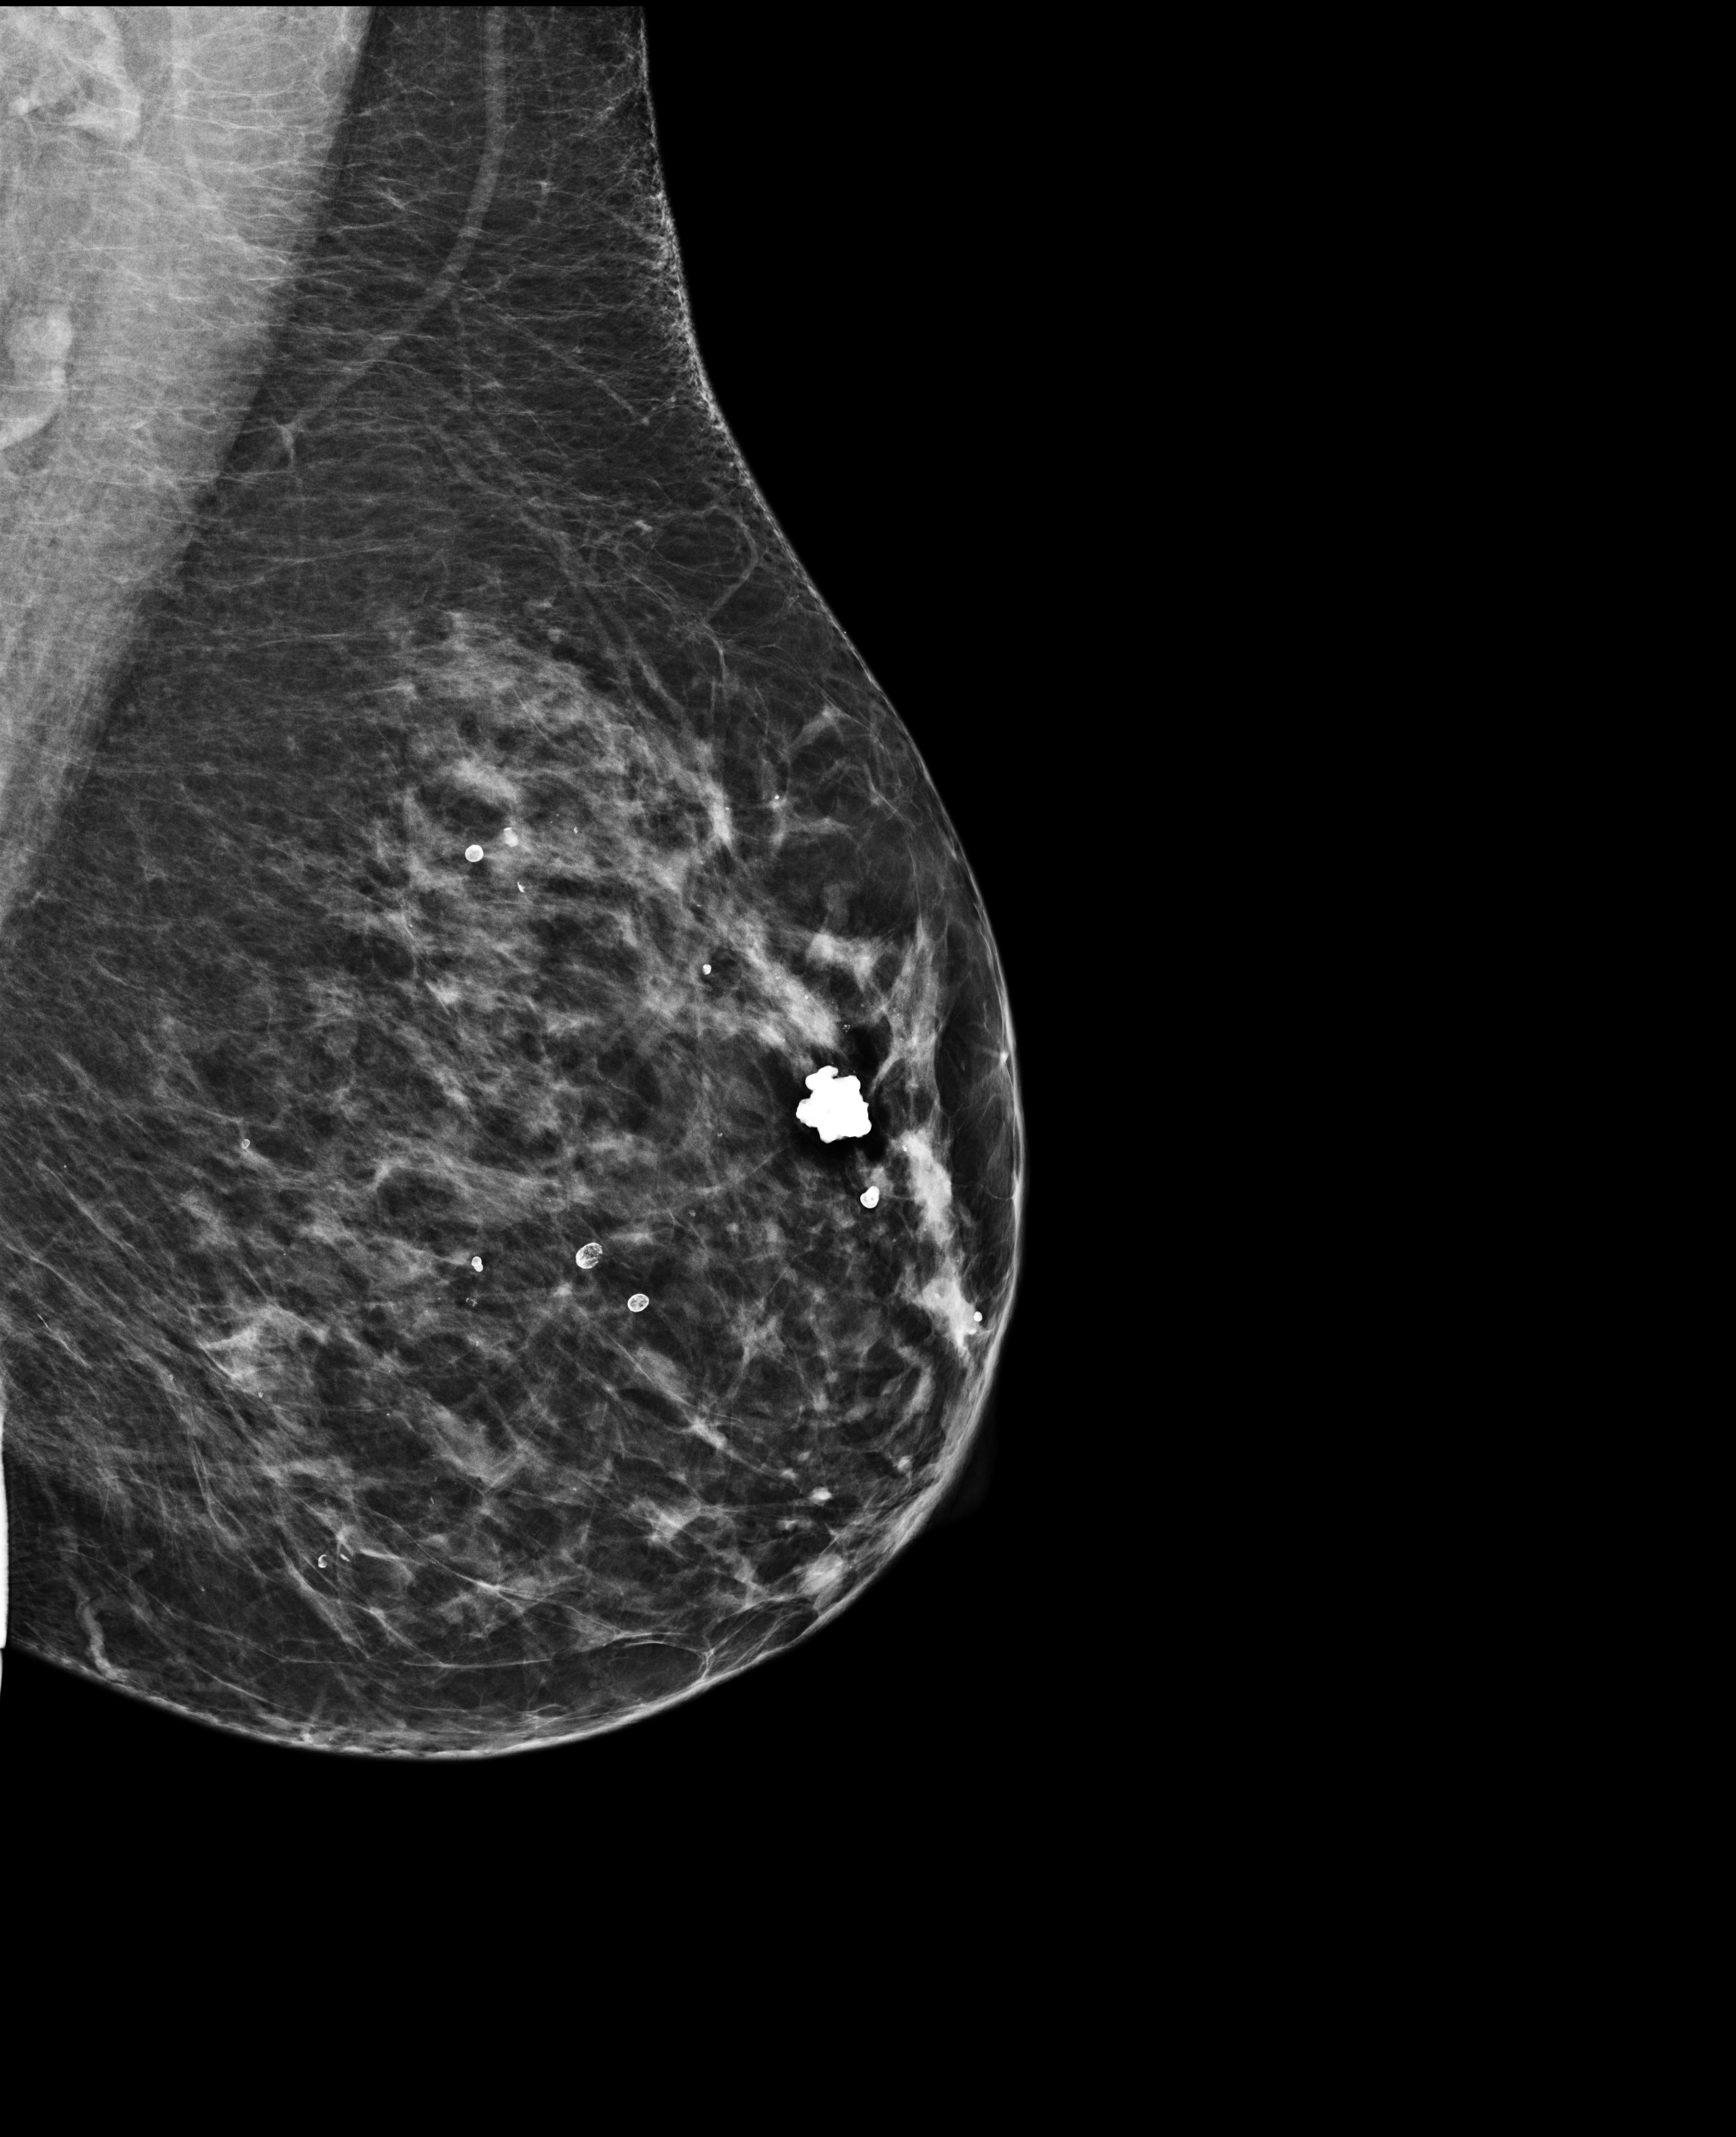
Annual screening mammography examination; system: Selenia Dimensions. Female patient, age 66 years.
Image type: full-field digital mammogram. Breast: left. Projection: mediolateral oblique (MLO) view.